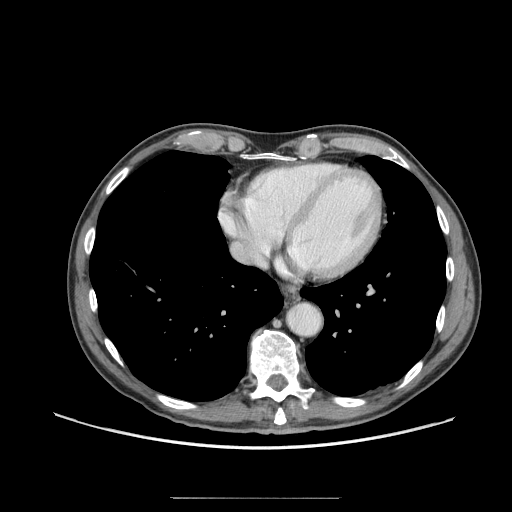
Contrast-enhanced abdominal CT (liver protocol), one axial slice. Position 70 of 71 along the scan axis. Reconstruction kernel STANDARD. 140 kVp. Soft-tissue window (W 400 / L 40 HU). 2.5 mm slice thickness. 512 × 512 image matrix. From the clinical record (not read from this slice): diagnosis: hepatocellular carcinoma (patient treated with transarterial chemoembolisation; whether this scan precedes or follows treatment is not stated here); TNM stage (as recorded): Stage-I; Child-Pugh class: A; tumour nodularity: uninodular; tumour size: 3.5 cm.
Annotated regions visible in this slice (semi-automatic segmentation, software-assisted and operator-edited):
- abdominal aorta: bounding box <288,304,320,335> (left, top, right, bottom; pixels)